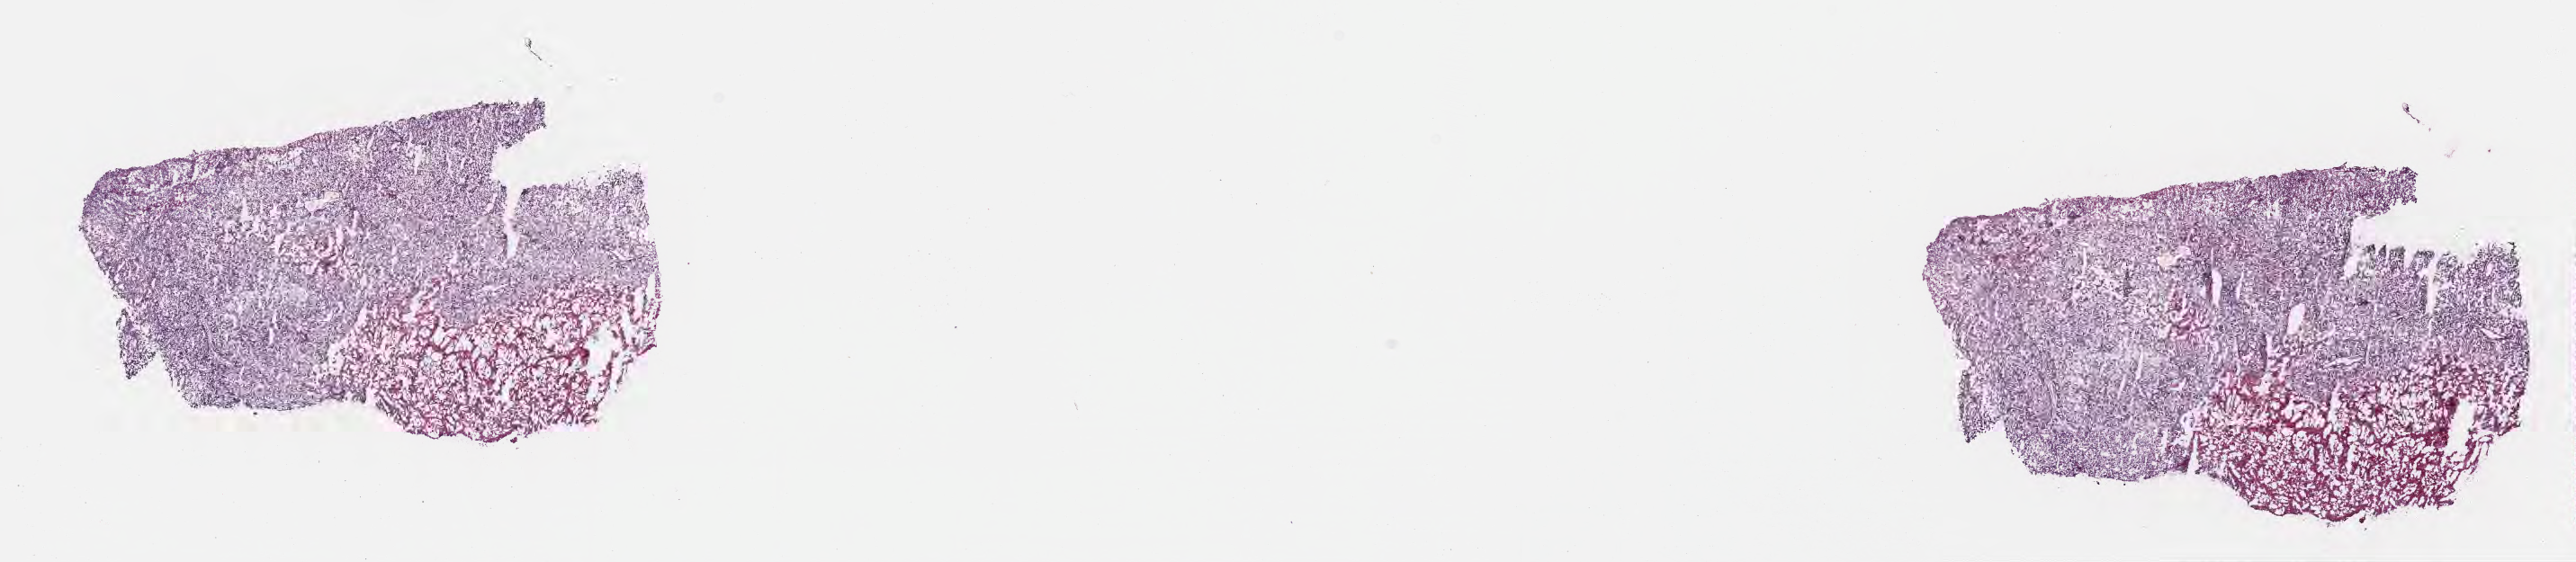
Whole-slide image, H&E stain, a low-resolution overview of the entire scanned area, about 23.1 x 5.1 mm; frozen section; metastatic tumor tissue, resected from brain. Female patient; age at initial diagnosis 65 years. Slide review estimates, as recorded: tumor cells 70%, tumor nuclei 95%, stromal cells 0%, necrosis 30%, normal cells 0%. Inflammatory infiltration, as recorded: lymphocyte infiltration 0%, monocyte infiltration 0%, neutrophil infiltration 0%.
- section: top of the tissue portion
- patient diagnosis (primary): Carcinoma, NOS